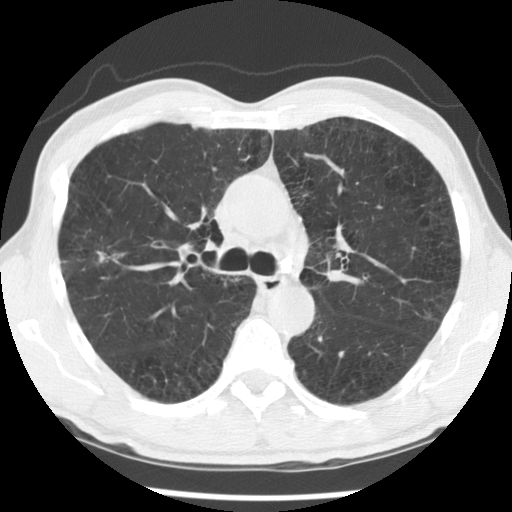
Low-dose screening chest CT, one axial slice; position 85 of 138 along the scan axis; reconstruction kernel STANDARD; 140 kVp; lung window (W 1500 / L -600 HU); 2.5 mm slice thickness; 512 × 512 image matrix, field of view 320 × 320 mm.
Outlined on this slice (outlined manually by an expert reader):
- lesion 1 (tumor, upper lobe of right lung): box from (x=97, y=251) to (x=110, y=263) px